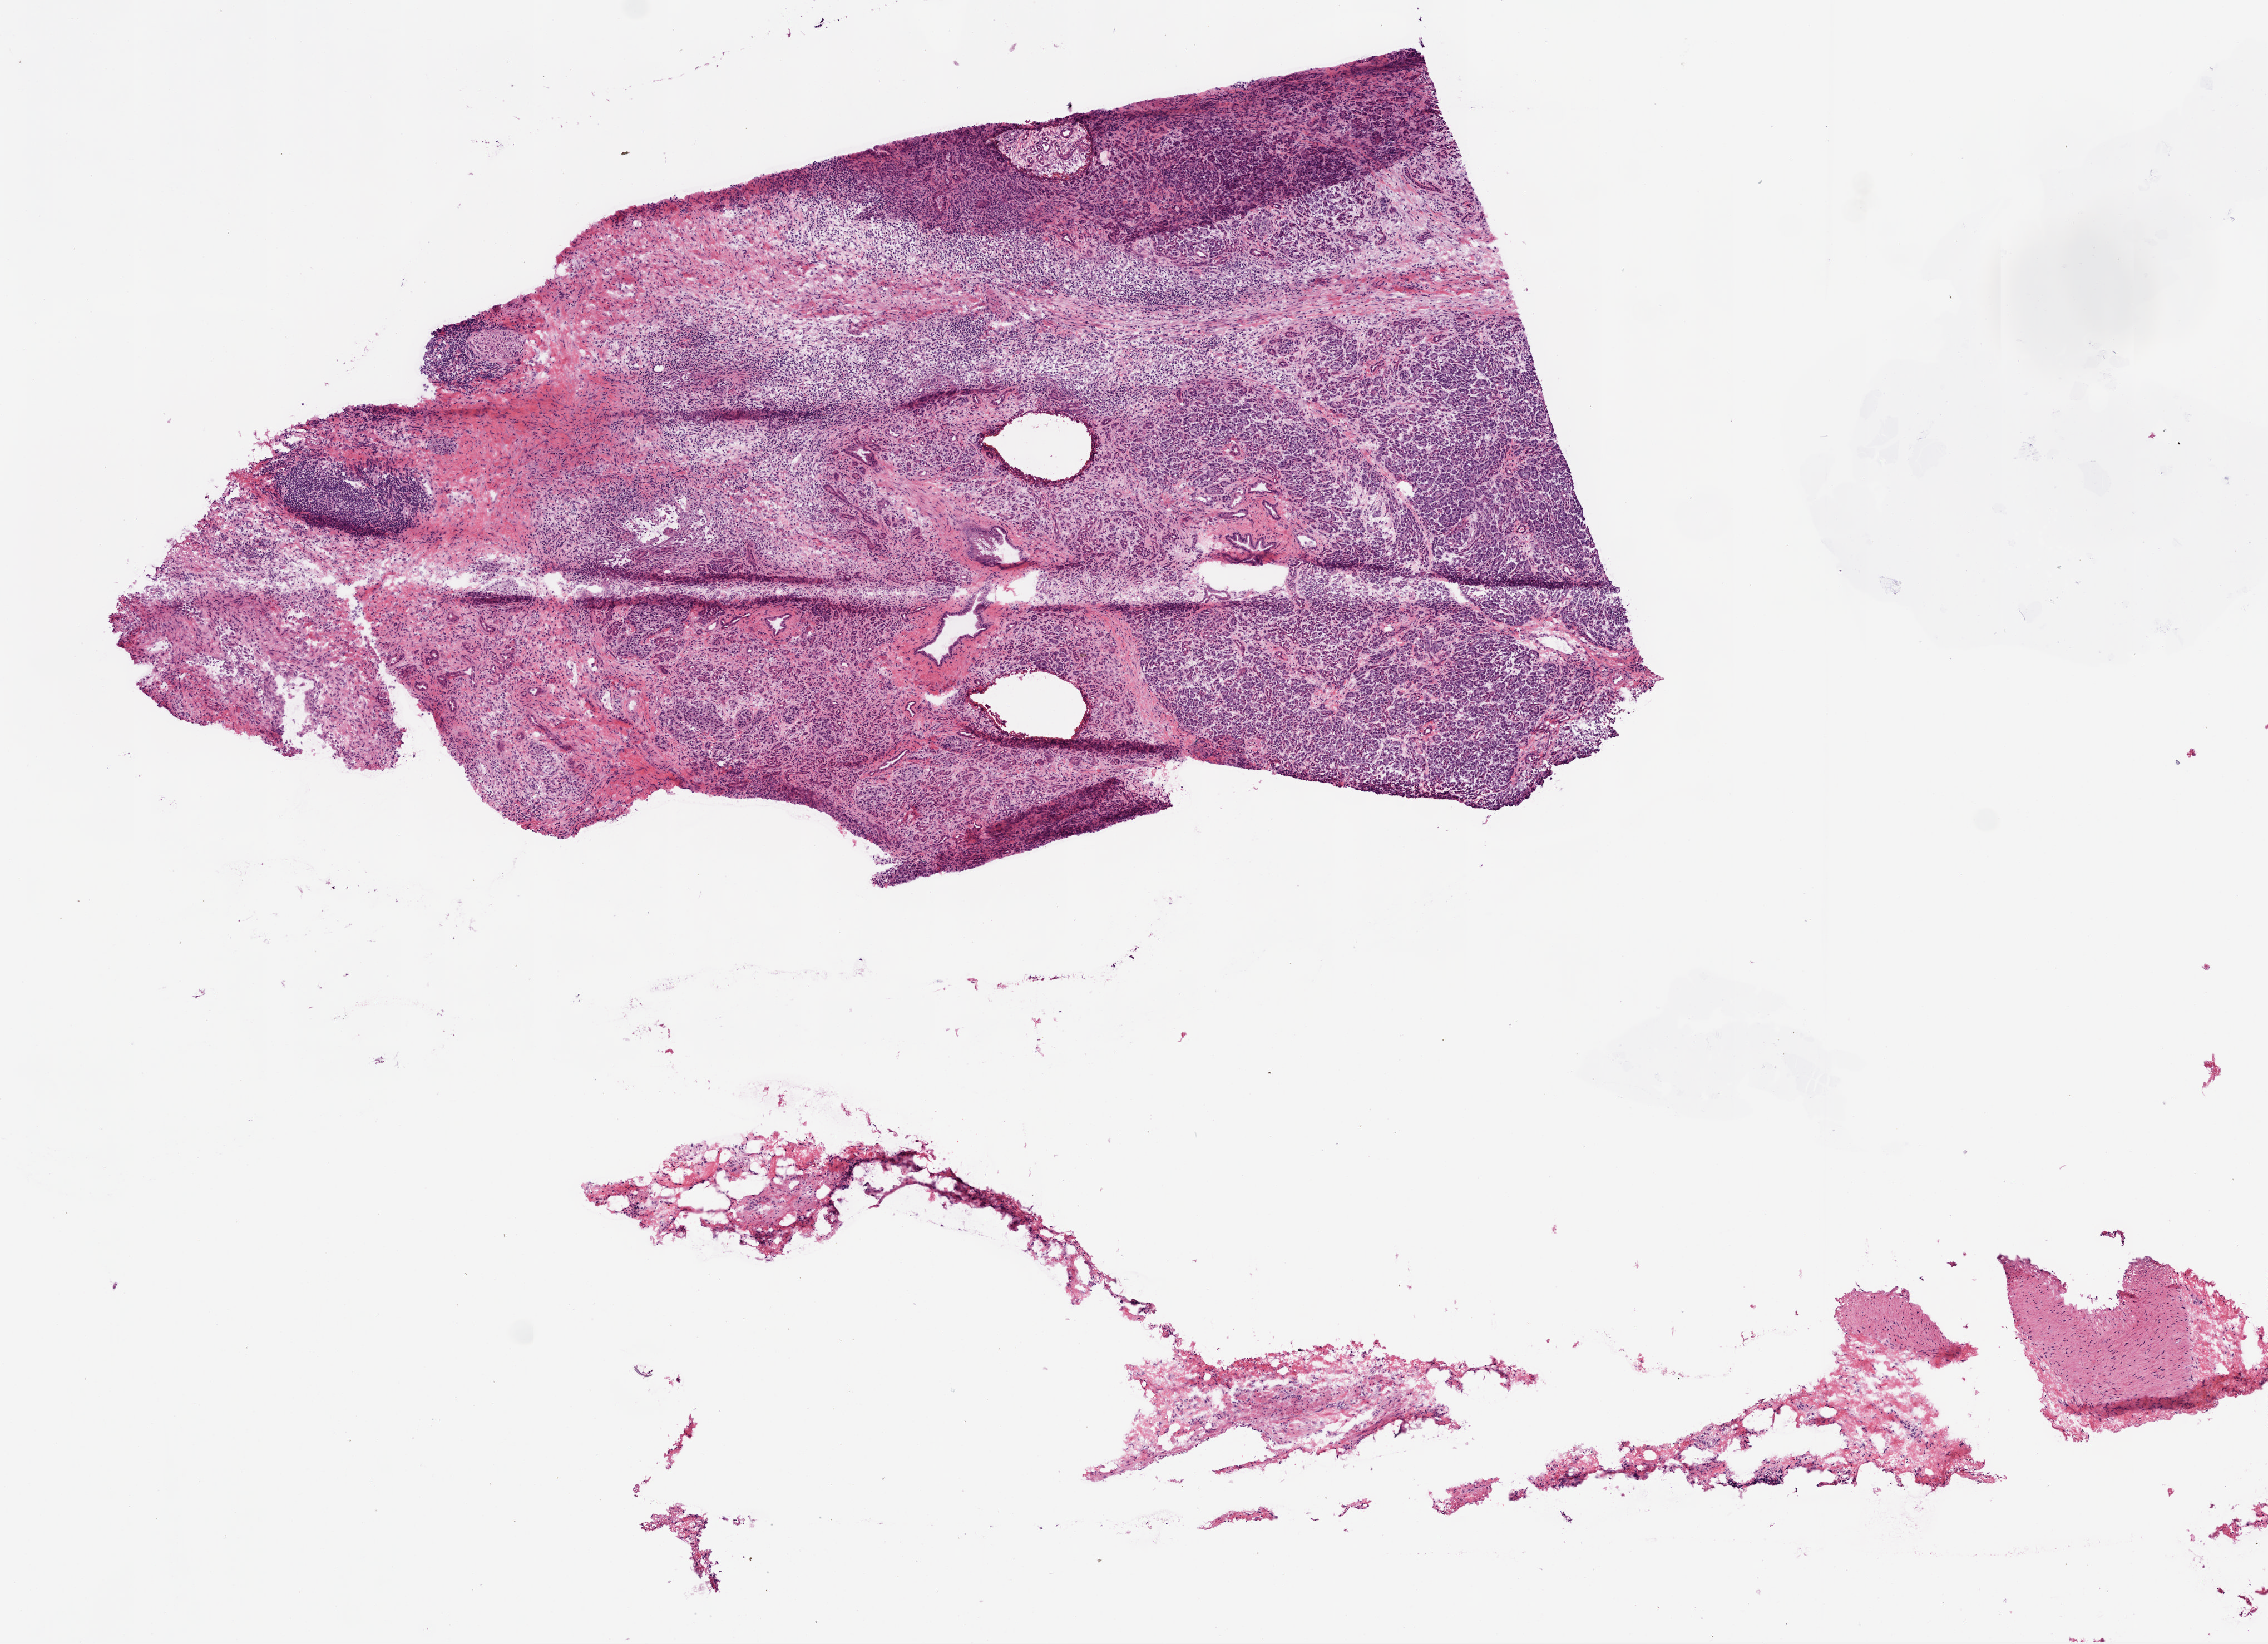
Whole-slide histology image, H&E-stained, a low-resolution overview of the entire scanned area, about 8.2 x 6.0 mm (from a 20x scan); frozen section from the top of the tissue portion; pancreas, primary tumour sample. Male, age 64 years at initial diagnosis. Histologic grade: G1 (well differentiated). Composition of this section per pathologist review: tumour cells 15%, tumour nuclei 15%, normal cells 85%, stromal cells 0%, necrosis 0%.
Diagnosis: Adenocarcinoma, NOS. AJCC pathologic stage: IIB (7th edition). Lymph nodes positive (case pathology): 9 of 17 examined.